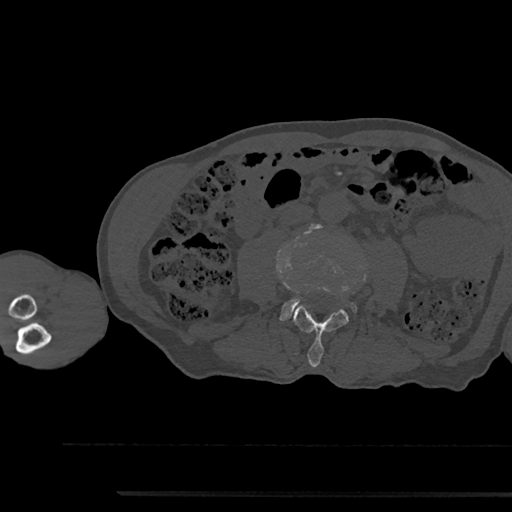
CT including the spine, one axial slice. Slice 455 of 797 in the series (ordered by position). Reconstruction kernel Br40s/3. Bone window (W 1800 / L 400 HU). 512 × 512 image matrix, field of view 367 × 367 mm. Patient: male, 79 years. Case-level facts recorded for this patient, not image findings: primary cancer: prostate.
Annotated regions visible in this slice (semi-automatic segmentation, software-assisted and operator-edited):
- L3 vertebra: bounding box [x1, y1, x2, y2] px = [293, 306, 349, 367]
- L4 vertebra: [281, 286, 356, 320]